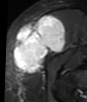
MRI of an extremity soft-tissue mass, one axial slice. Position 22 of 48 along the scan axis. STIR. MR volume resampled by the dataset authors to the PET/CT grid (not the native acquisition matrix). 3.27 mm slice thickness. 87 × 102 image matrix, field of view 85 × 100 mm. Female patient. Case-level facts recorded for this patient, not image findings: histological type: synovial sarcoma; grade: intermediate; site of the primary tumour: right thigh.
Structures marked on this image (expert contour drawn on MRI and transferred to this co-registered scan by the dataset authors):
- gross tumour volume including surrounding oedema: box from (x=13, y=15) to (x=66, y=73) px
- gross tumour volume (mass): (x=13, y=15)–(x=66, y=73)